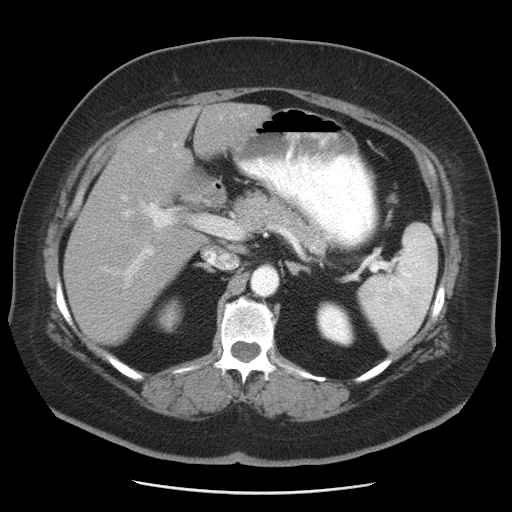
Contrast-enhanced abdominal CT, one axial slice; reconstruction kernel STANDARD; 120 kVp; soft-tissue window (W 400 / L 40 HU); 5 mm slice thickness; 512 × 512 image matrix. Female patient, age 52 years. From the clinical record (not read from this slice): diagnosis: colorectal cancer liver metastases, imaged before liver resection; multiple liver metastases: yes; largest metastasis: 2.5 cm; disease in both lobes: yes.
Annotated regions visible in this slice (manually delineated by an expert):
- liver: bounding box [x1, y1, x2, y2] px = [64, 104, 270, 345]
- planned liver remnant (the part of the liver to remain after resection): [64, 196, 207, 345]
- portal vein (with intrahepatic branches): [100, 134, 217, 286]